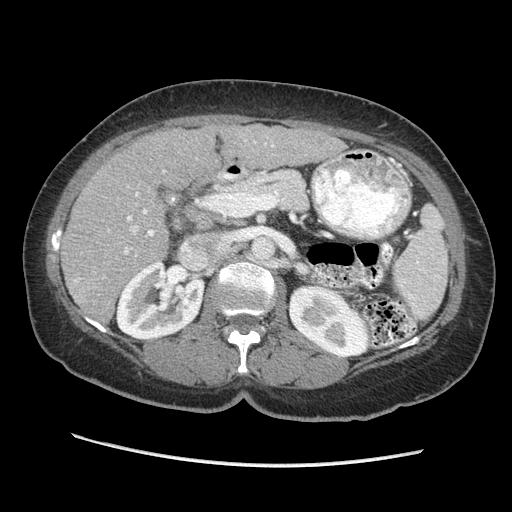
Contrast-enhanced abdominal CT (liver protocol), one axial slice. Slice 120 of 170 in the series (ordered by position). Soft-tissue window (W 400 / L 40 HU). 2.5 mm slice thickness. 512 × 512 image matrix. Case-level facts recorded for this patient, not image findings: diagnosis: hepatocellular carcinoma (patient treated with transarterial chemoembolisation; whether this scan precedes or follows treatment is not stated here); TNM stage (as recorded): Stage-II; Child-Pugh class: A; tumour differentiation: no biopsy; tumour nodularity: multinodular.
Annotated regions visible in this slice (semi-automatic segmentation, software-assisted and operator-edited):
- liver parenchyma outside the tumour (the mass and vessels are separate outlines, so this box may not span the whole liver): box from (x=61, y=122) to (x=345, y=320) px
- liver vessels: (x=74, y=140)–(x=274, y=282)